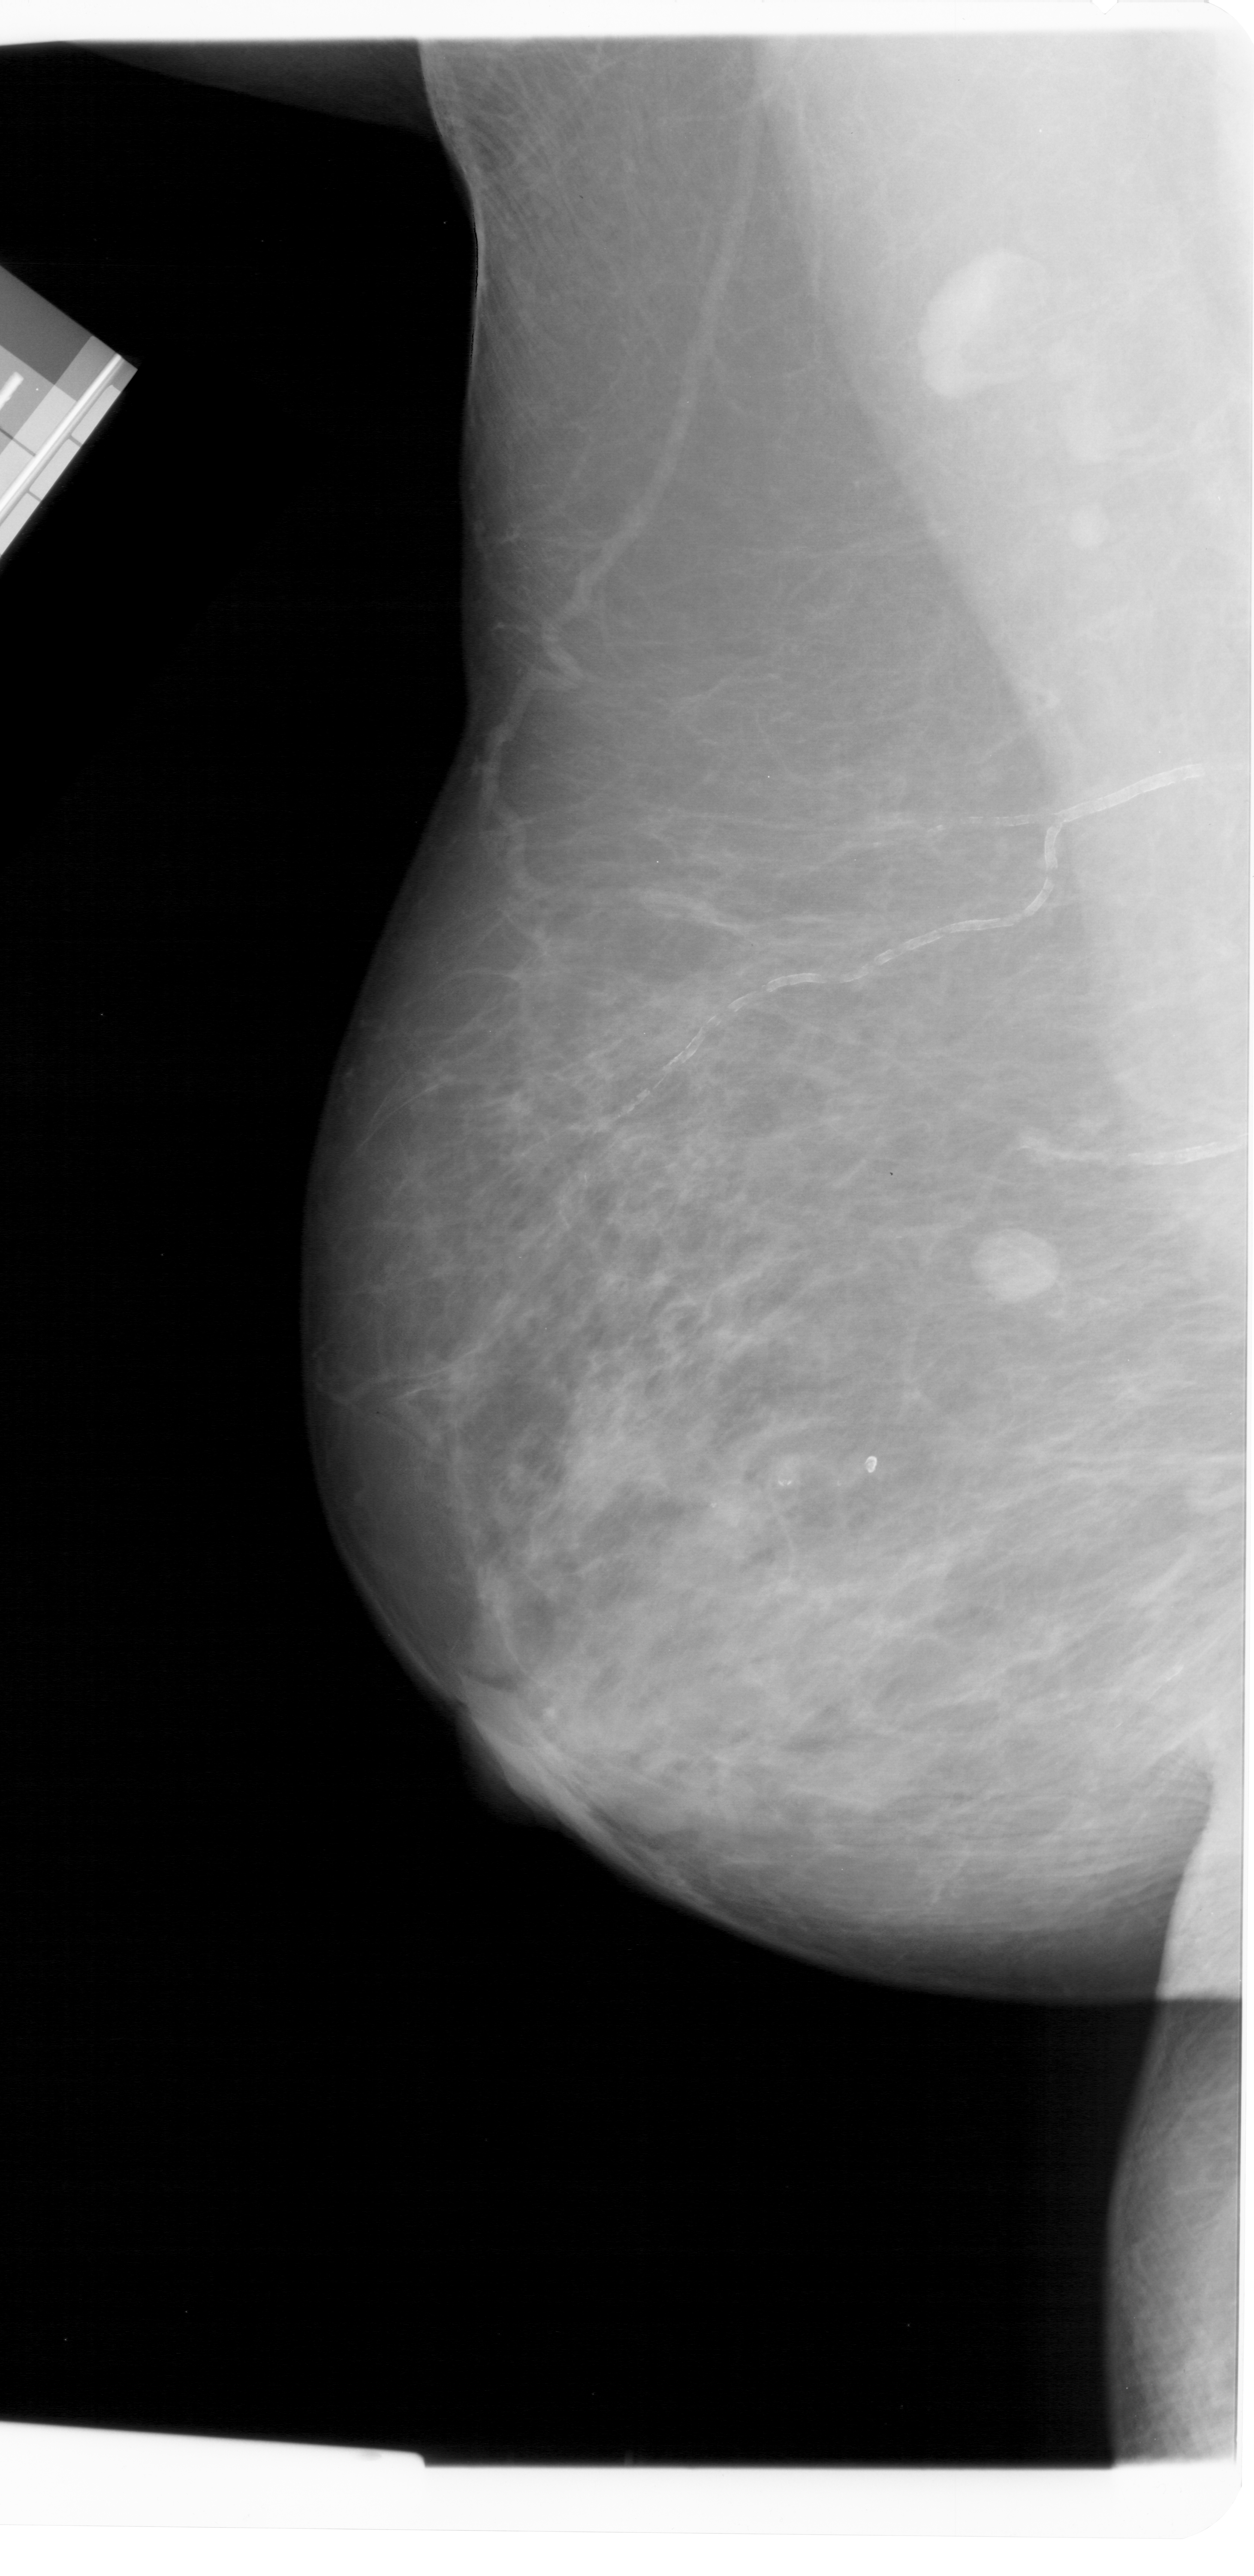
Digitized screen-film mammogram; left breast; MLO view; 1254 × 2576 image matrix.
Marked abnormalities (boxes around the expert regions of interest):
- mass, shape round, margins circumscribed; BI-RADS assessment category 3; subtlety rating 4 on a 1 (subtle) to 5 (obvious) scale; pathology (as recorded): benign: bounding box (x1, y1, x2, y2) in pixels: (971, 1227, 1067, 1309)